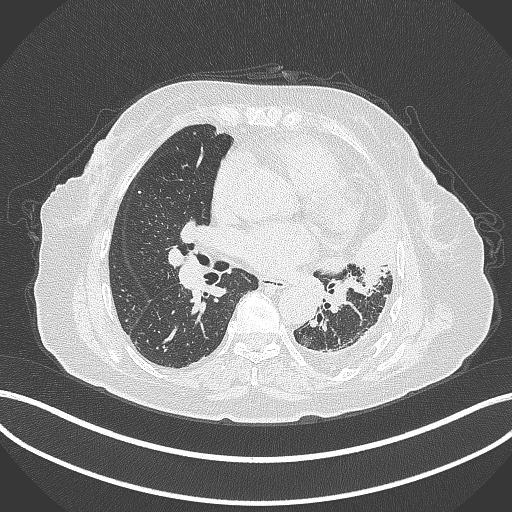
Chest CT, one axial slice; position 181 of 399 along the scan axis; 120 kVp; lung window (W 1500 / L -600 HU); 1 mm slice thickness; 512 × 512 image matrix, field of view 400 × 400 mm. Patient: female, 75 years. Case-level facts recorded for this patient, not image findings: clinical TNM (as recorded): T3 N3 M1.
Outlined on this slice (bounding box drawn by a radiologist):
- lung tumour (recorded histology: adenocarcinoma): bounding box (x1, y1, x2, y2) in pixels: (310, 217, 398, 282)